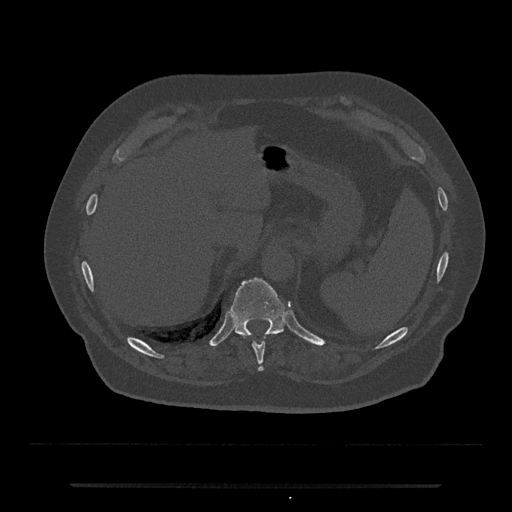
CT including the spine, one axial slice; position 673 of 797 along the scan axis; reconstruction kernel Br40s/3; 120 kVp; bone window (W 1800 / L 400 HU); 512 × 512 image matrix. Male patient, age 80 years. From the clinical record (not read from this slice): primary cancer: prostate.
Outlined on this slice (semi-automatically segmented with operator editing):
- T10 vertebra: bounding box <252,342,265,371> (left, top, right, bottom; pixels)
- T11 vertebra: <231,278,285,337>